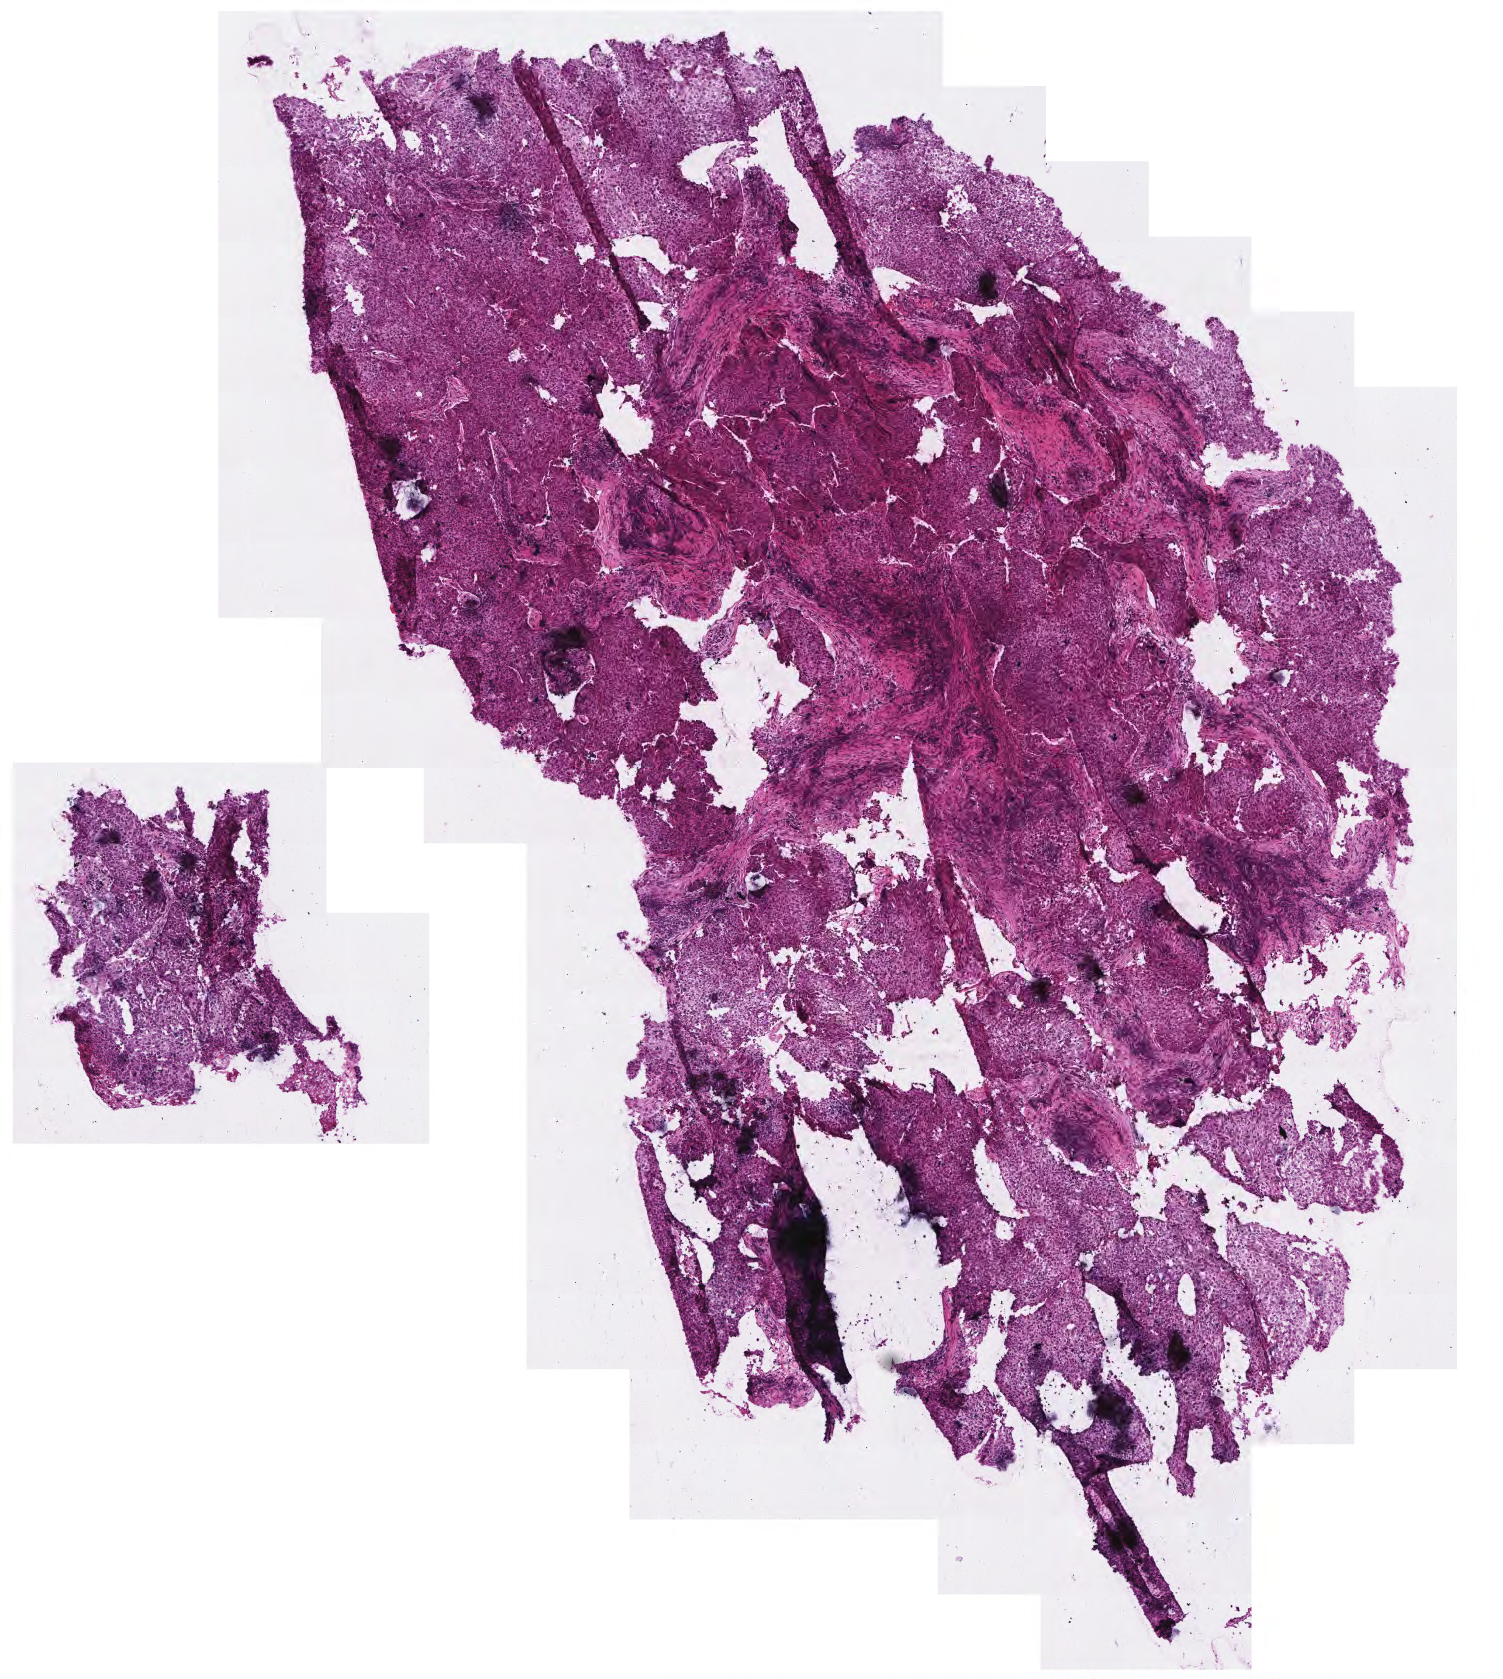
Whole-slide histology image, Hematoxylin and eosin (H&E) stained — low-resolution overview of the scanned area, about 3.0 x 3.4 mm; frozen section; head and neck, primary tumour sample. Patient: male, age at initial diagnosis 59 years. Histologic grade: G3 (poorly differentiated). Pathologist review of this section (percent, as recorded): tumour cells 90%, tumour nuclei 85%, normal cells 0%, stromal cells 10%, necrosis 0%.
* pathologic diagnosis: Squamous cell carcinoma, NOS (base of tongue, NOS)